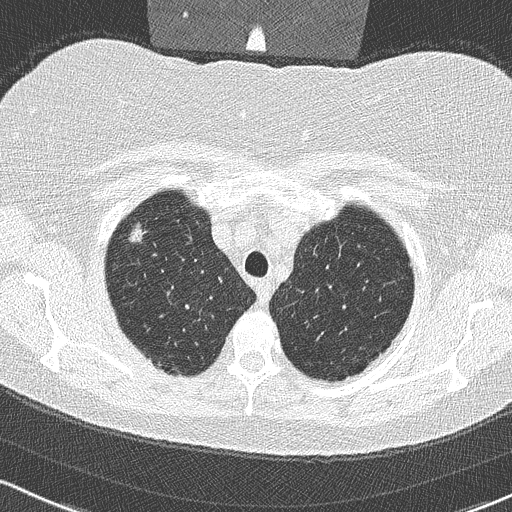
Low-dose screening chest CT, one axial slice; position 268 of 315 along the scan axis; 120 kVp; lung window (W 1500 / L -600 HU); 512 × 512 image matrix, field of view 320 × 320 mm.
Annotated regions visible in this slice (expert manual segmentation):
- lesion 1 (tumor, upper lobe of right lung): box from (x=128, y=221) to (x=147, y=242) px